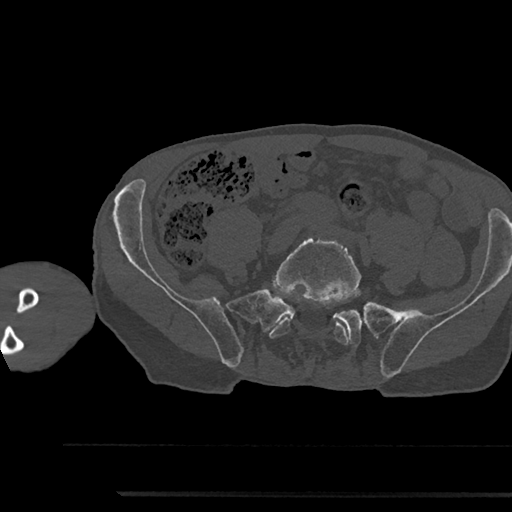
CT including the spine, one axial slice. Reconstruction kernel Br40s/3. Bone window (W 1800 / L 400 HU). 0.5 mm slice thickness. 512 × 512 image matrix, field of view 367 × 367 mm. Patient: male, 79 years. From the clinical record (not read from this slice): primary cancer: prostate.
Annotated regions visible in this slice (semi-automatic segmentation, software-assisted and operator-edited):
- L5 vertebra: box from (x=269, y=235) to (x=361, y=345) px